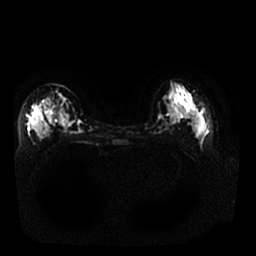
Breast MRI, one axial slice. Slice 10 of 25 in the series (ordered by position). Diffusion-weighted series; image 2 of 4 stored at this slice position (different b-values; order by instance number). 1.5 T. 4 mm slice thickness. 256 × 256 image matrix. Female patient.
Structures marked on this image (outlined manually by an expert reader):
- tumour on diffusion-weighted imaging: bounding box (x1, y1, x2, y2) in pixels: (29, 106, 41, 132)